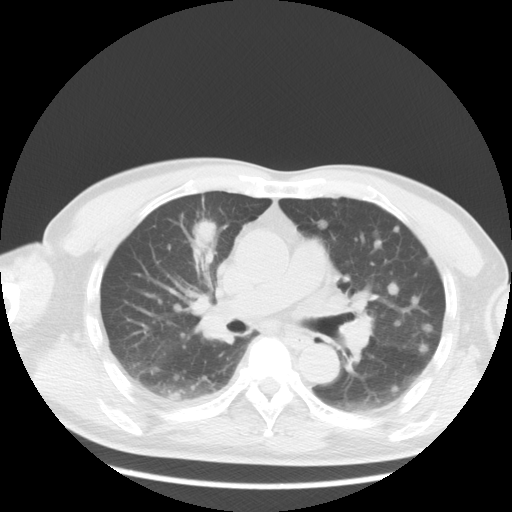
Chest CT, one axial slice. Position 13 of 35 along the scan axis. 120 kVp. Lung window (W 1500 / L -600 HU). 5 mm slice thickness. 512 × 512 image matrix, field of view 369 × 369 mm. Patient: male, 57 years. Case-level facts recorded for this patient, not image findings: clinical TNM (as recorded): T2 N3 M1a.
Outlined on this slice (rectangle marked by the reading radiologist):
- lung tumour (recorded histology: adenocarcinoma): bounding box <194,216,215,247> (left, top, right, bottom; pixels)